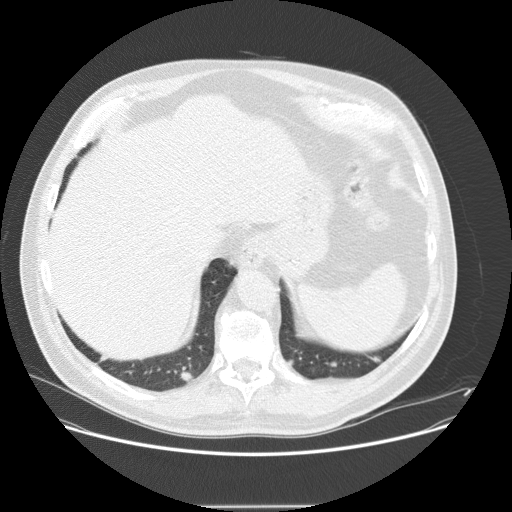
Low-dose screening chest CT, axial slice; baseline screening round; lung window (W 1500 / L -600 HU); standard (soft-tissue) reconstruction kernel (STANDARD); slice 109 of 143 in the series; 512 × 512 image matrix, field of view 400 × 400 mm. Male participant, aged 61 years at enrolment. Current smoker at enrolment.
- Lesion marked by an expert reader, bounding box <164,360,203,397> (left, top, right, bottom; pixels).
- The screening reader recorded 2 non-calcified nodules or masses ≥4 mm on this exam (left lower lobe, right lower lobe); which of them this box marks is not recorded.
- Later outcome: lung cancer diagnosed 41 days after this screen — bronchiolo-alveolar carcinoma, mucinous, right lower lobe, well differentiated (G1), stage IV (AJCC 6th edition), 23 mm at pathology.